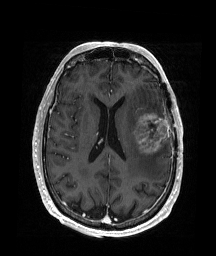
Brain MRI from a brain-tumour surgery series, one axial slice; position 80 of 176 along the scan axis; T1-weighted post-contrast; 216 × 256 image matrix. From the clinical record (not read from this slice): histopathology: Glioblastoma; WHO grade: 4; IDH mutation: no; tumour location: Left Frontal.
Structures marked on this image (outlined manually by an expert reader):
- tumour: box from (x=132, y=113) to (x=169, y=155) px